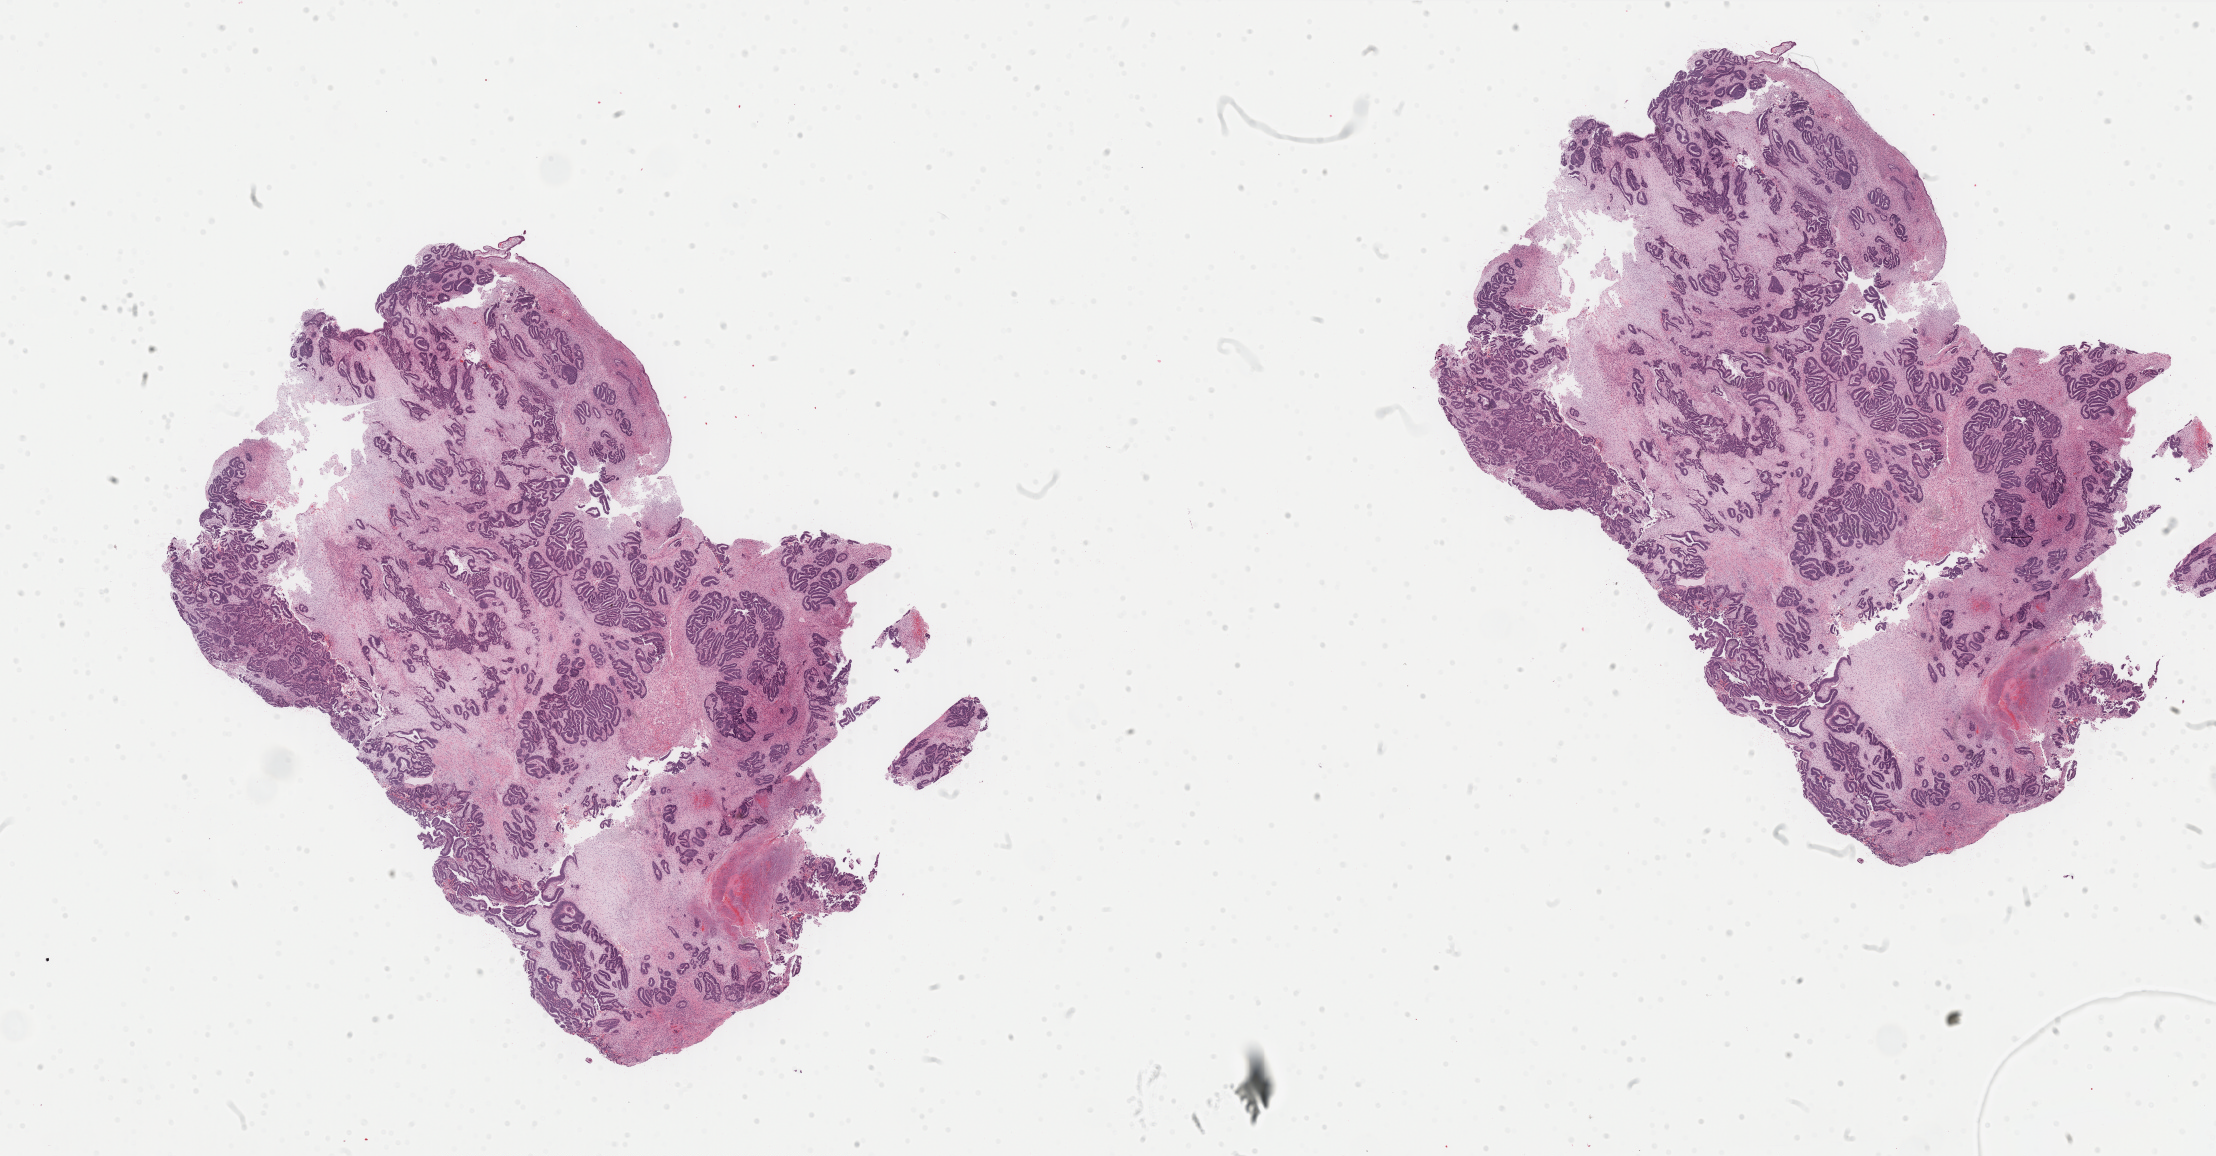
H&E whole-slide image, a low-resolution overview of the entire scanned area, about 35.1 x 18.3 mm (from a 40x scan), formalin-fixed paraffin-embedded (FFPE) diagnostic section, uterus, primary tumour sample. Female patient; age at initial diagnosis 61 years. Histologic grade: G3 (poorly differentiated).
* histologic diagnosis: Endometrioid adenocarcinoma, NOS (endometrium)
* lymph nodes positive (case pathology): 0 of 22 examined
* FIGO stage: IA